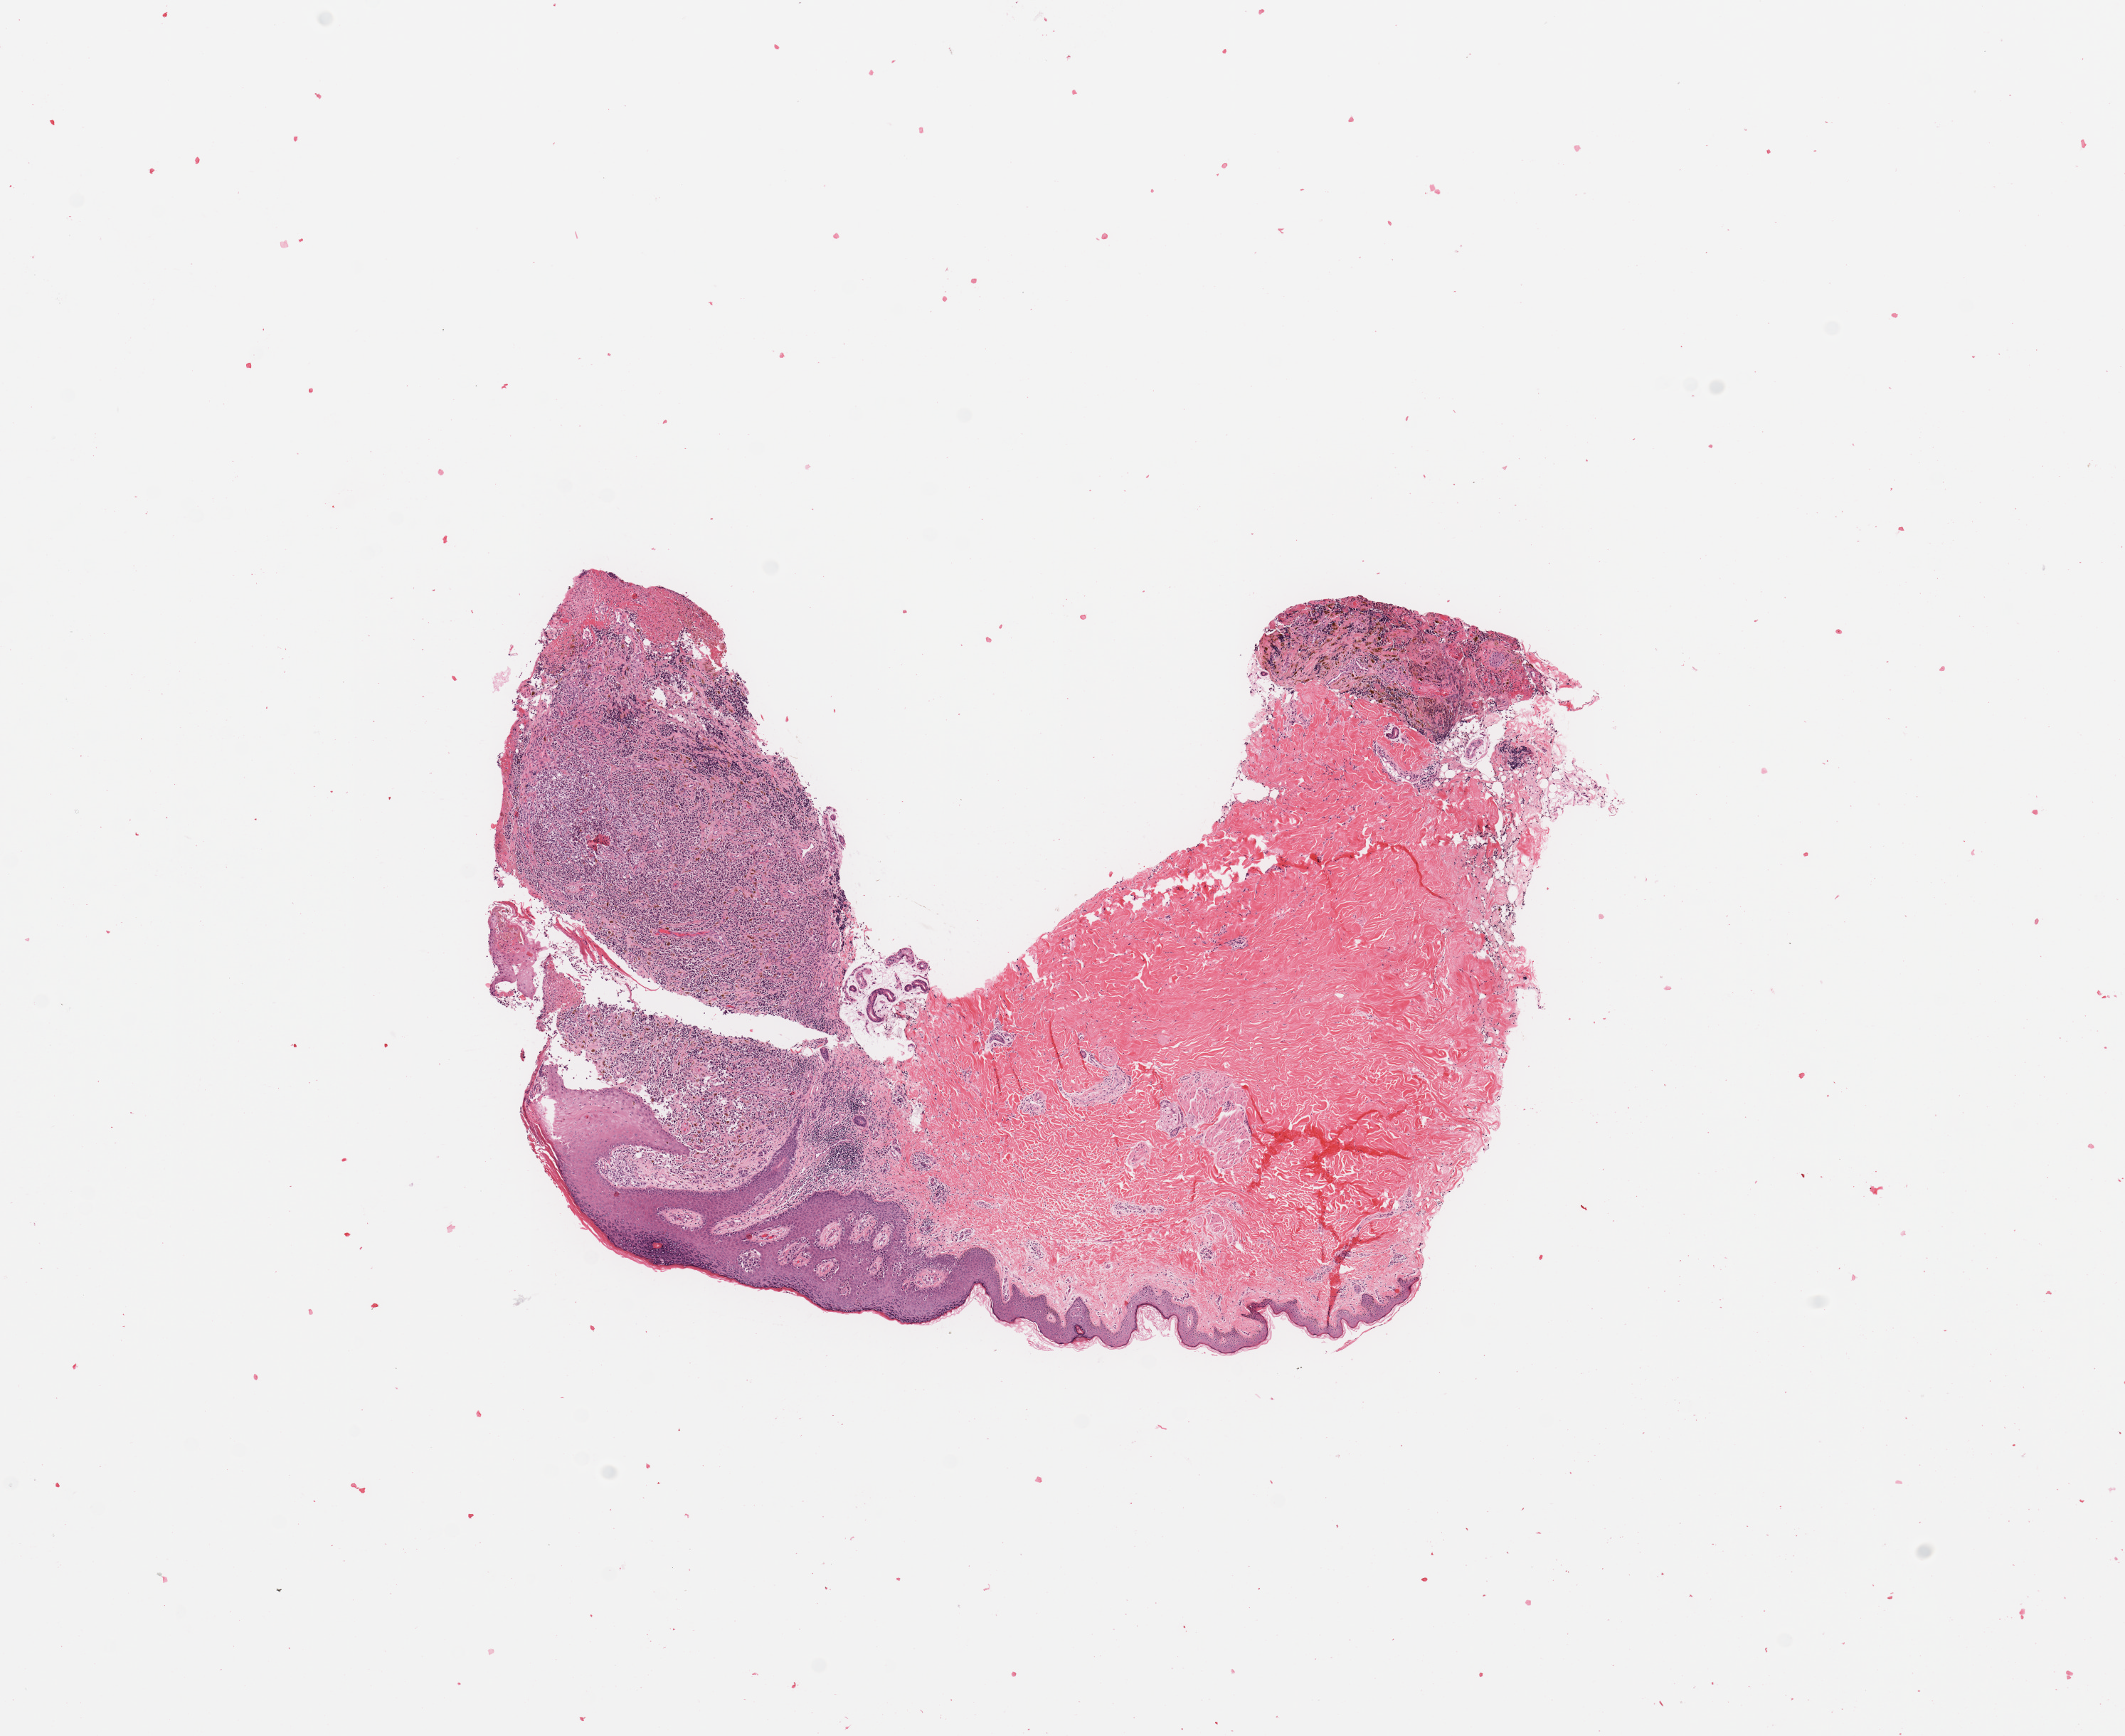
H&E whole-slide image — a low-resolution overview of the entire scanned area, about 11.8 x 9.6 mm (from a 20x scan), melanoma tumour tissue; sampled site not recorded. 49-year-old female patient.
- histologic diagnosis: Malignant melanoma, NOS
- primary tumour site (as recorded): trunk